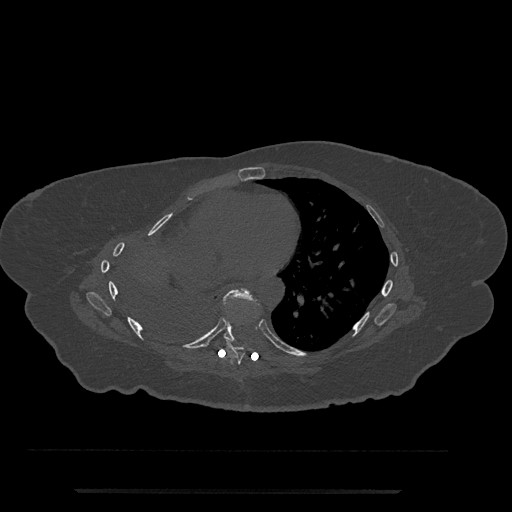
CT including the spine, one axial slice; slice 419 of 797 in the series (ordered by position); 120 kVp; bone window (W 1800 / L 400 HU); 512 × 512 image matrix, field of view 440 × 440 mm. Patient: female, 51 years. Case-level facts recorded for this patient, not image findings: primary cancer: neuro; vertebrae with lytic lesions (as recorded): T8.
Outlined on this slice (semi-automatically segmented with operator editing):
- T7 vertebra: box from (x=224, y=340) to (x=245, y=365) px
- T8 vertebra: (x=223, y=288)–(x=257, y=342)